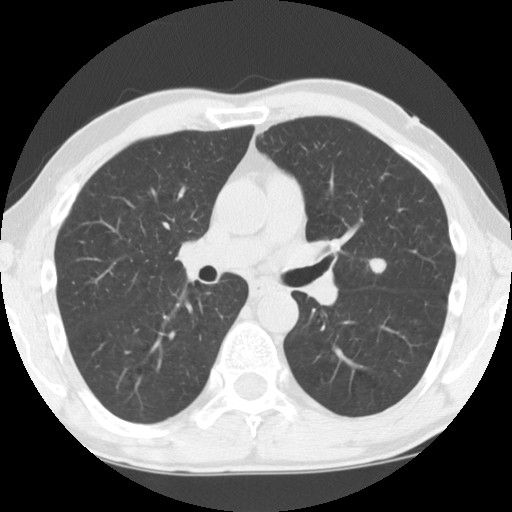
Axial slice from a low-dose chest CT screening exam. First (baseline) screen. Lung window (W 1500 / L -600 HU). 2.5 mm slice thickness. Standard (soft-tissue) reconstruction kernel (STANDARD). Male, age 55 years at enrolment. Current smoker at enrolment.
Expert reader's lesion annotation, bounding box <350,246,400,286> (left, top, right, bottom; pixels). The screening reader recorded 5 non-calcified nodules or masses ≥4 mm on this exam (left upper lobe, left upper lobe, right upper lobe, right upper lobe, left upper lobe); which of them this box marks is not recorded. Official screen result: positive, change unspecified: nodule(s) >= 4 mm or enlarging nodule(s), mass(es), or other non-specific abnormalities suspicious for lung cancer. Later outcome: lung cancer diagnosed 59 days after this screen — large cell neuroendocrine carcinoma, left upper lobe, stage IA (AJCC 6th edition), 15 mm at pathology.